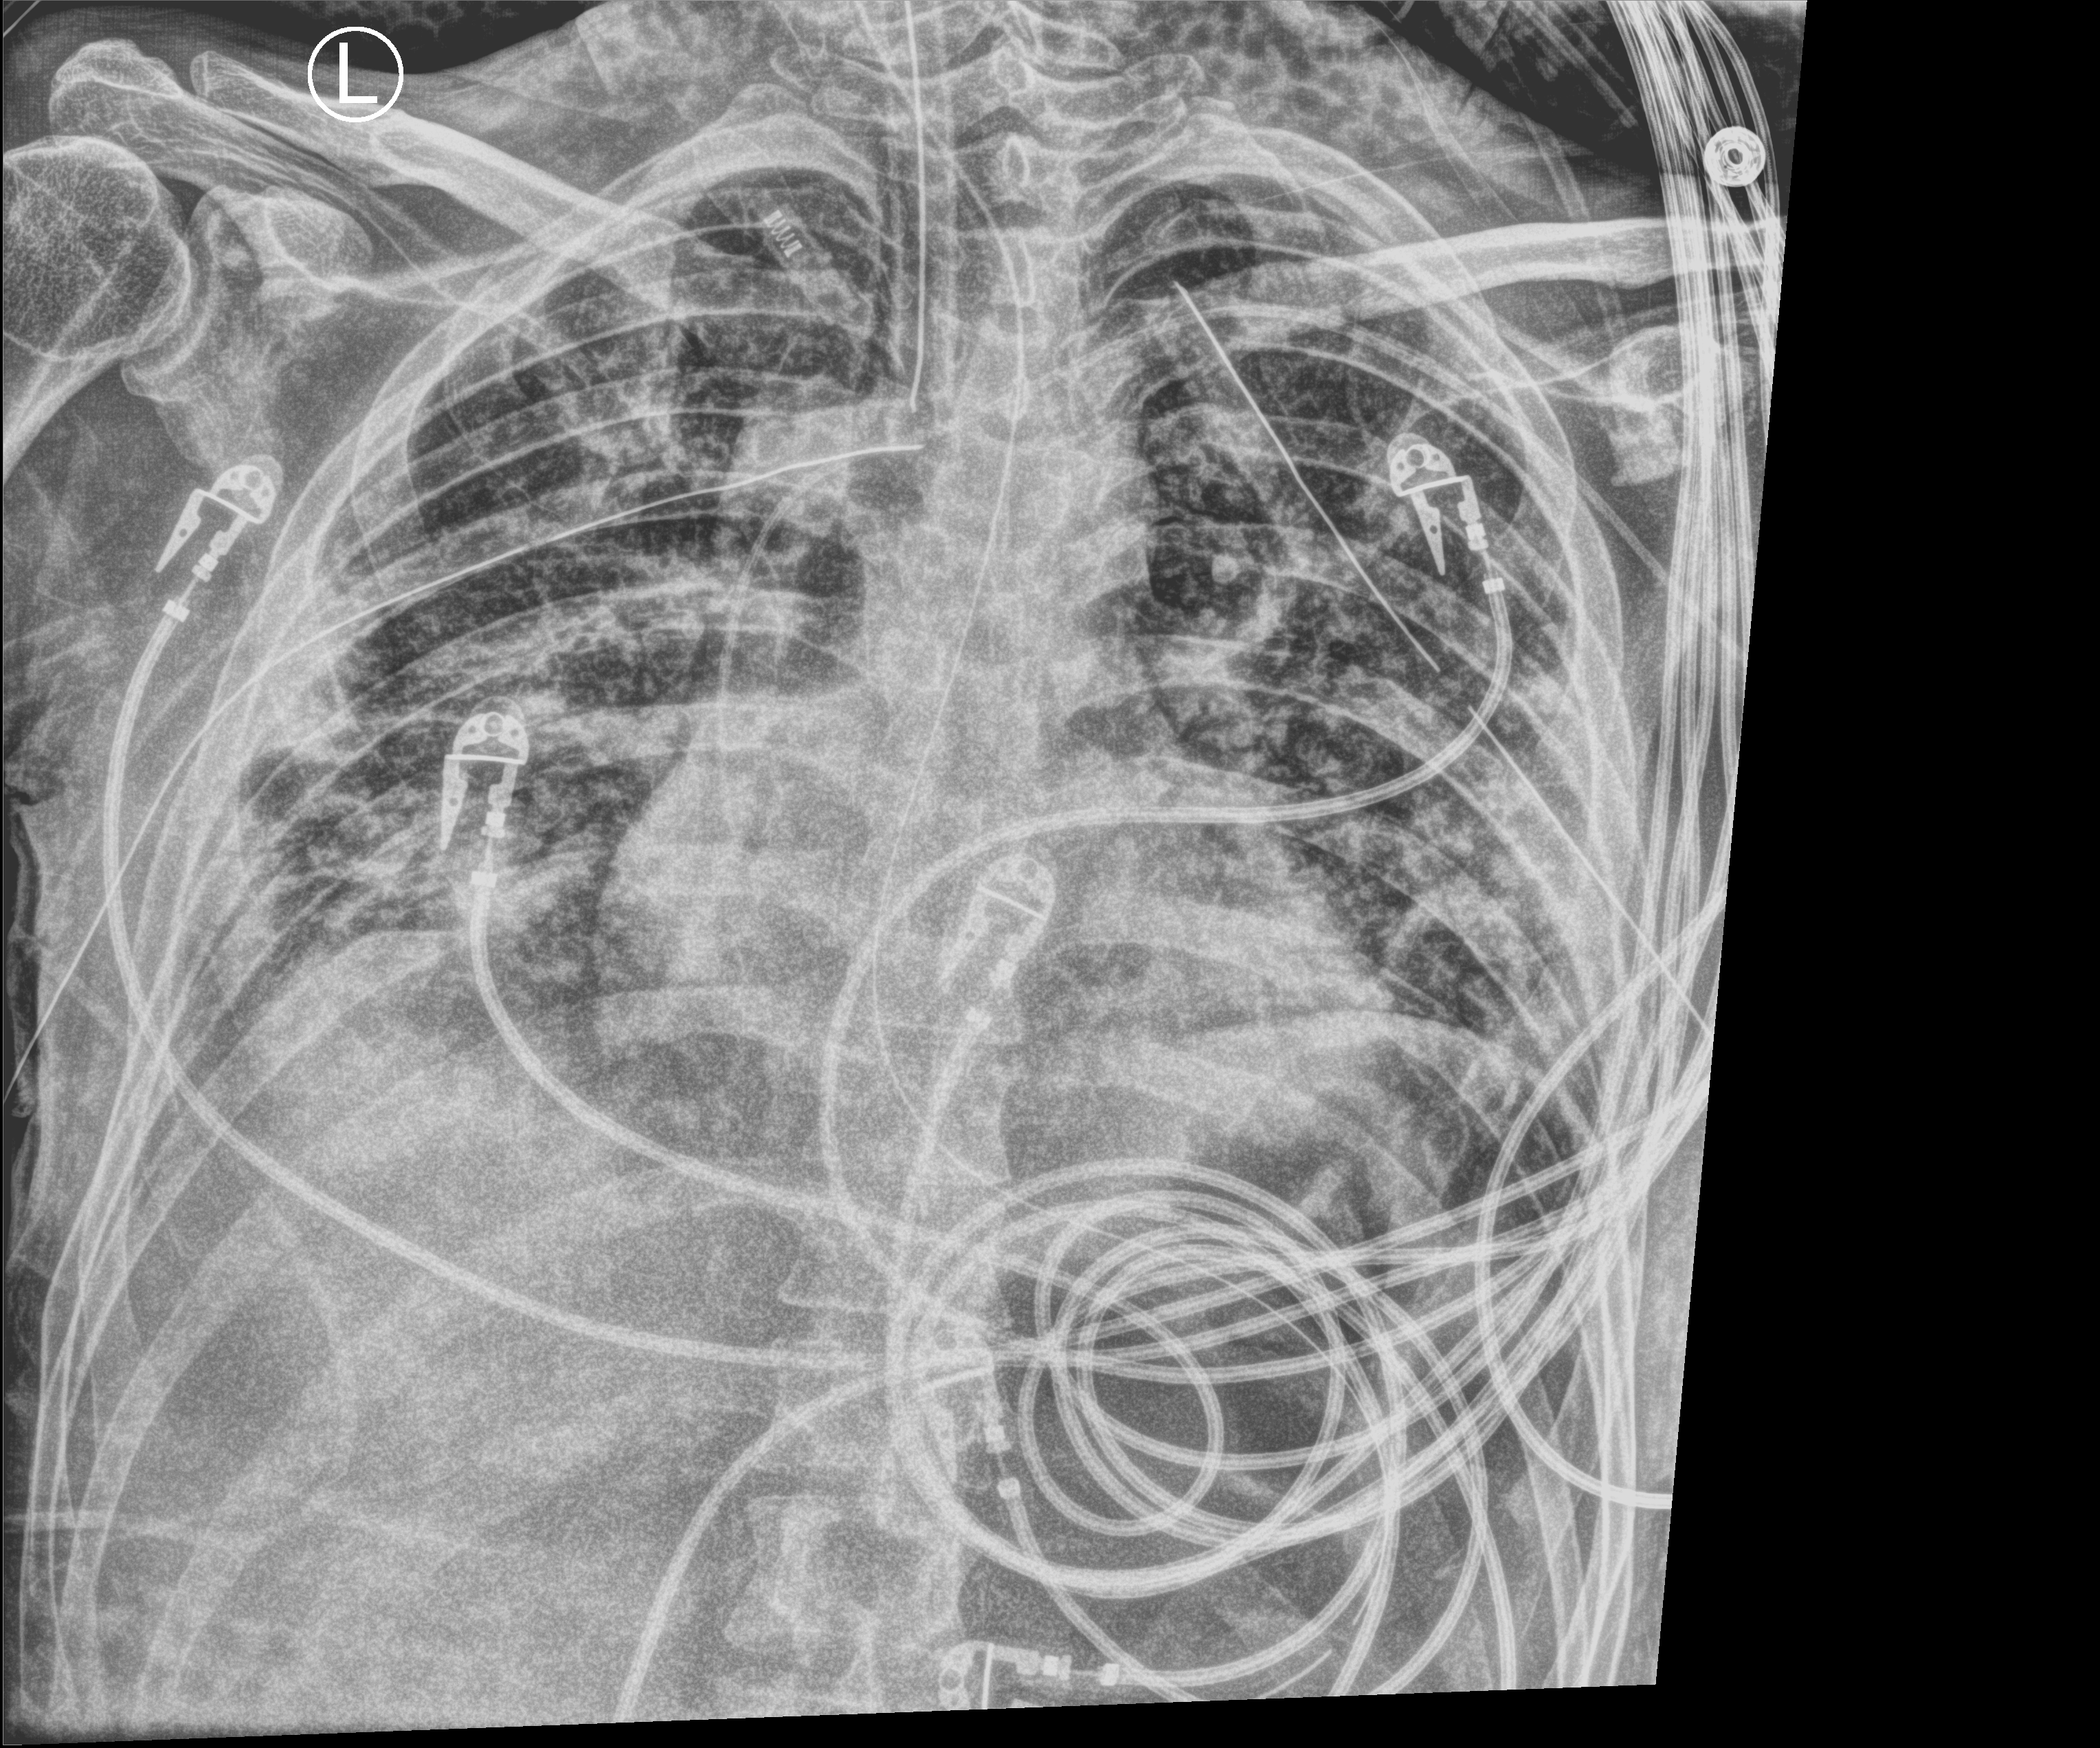
Bedside chest radiograph (computed radiography); anteroposterior (AP) projection. Patient hospitalised with COVID-19; male, aged 18–59 years.
Hospital-stay facts (about this admission, not read from this image; timing relative to this image not recorded): length of hospital stay: 96 days.